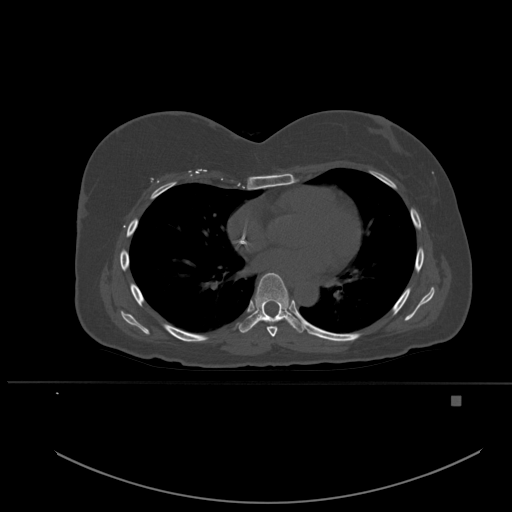
CT including the spine, one axial slice; slice 340 of 651 in the series (ordered by position); bone window (W 1800 / L 400 HU); 512 × 512 image matrix, field of view 443 × 443 mm. Patient: female, 49 years. Case-level facts recorded for this patient, not image findings: primary cancer: breast; vertebrae with lytic lesions (as recorded): L3, T12, L4.
Outlined on this slice (semi-automatic segmentation, software-assisted and operator-edited):
- T6 vertebra: bounding box (x1, y1, x2, y2) in pixels: (266, 326, 278, 337)
- T7 vertebra: (239, 273, 304, 333)